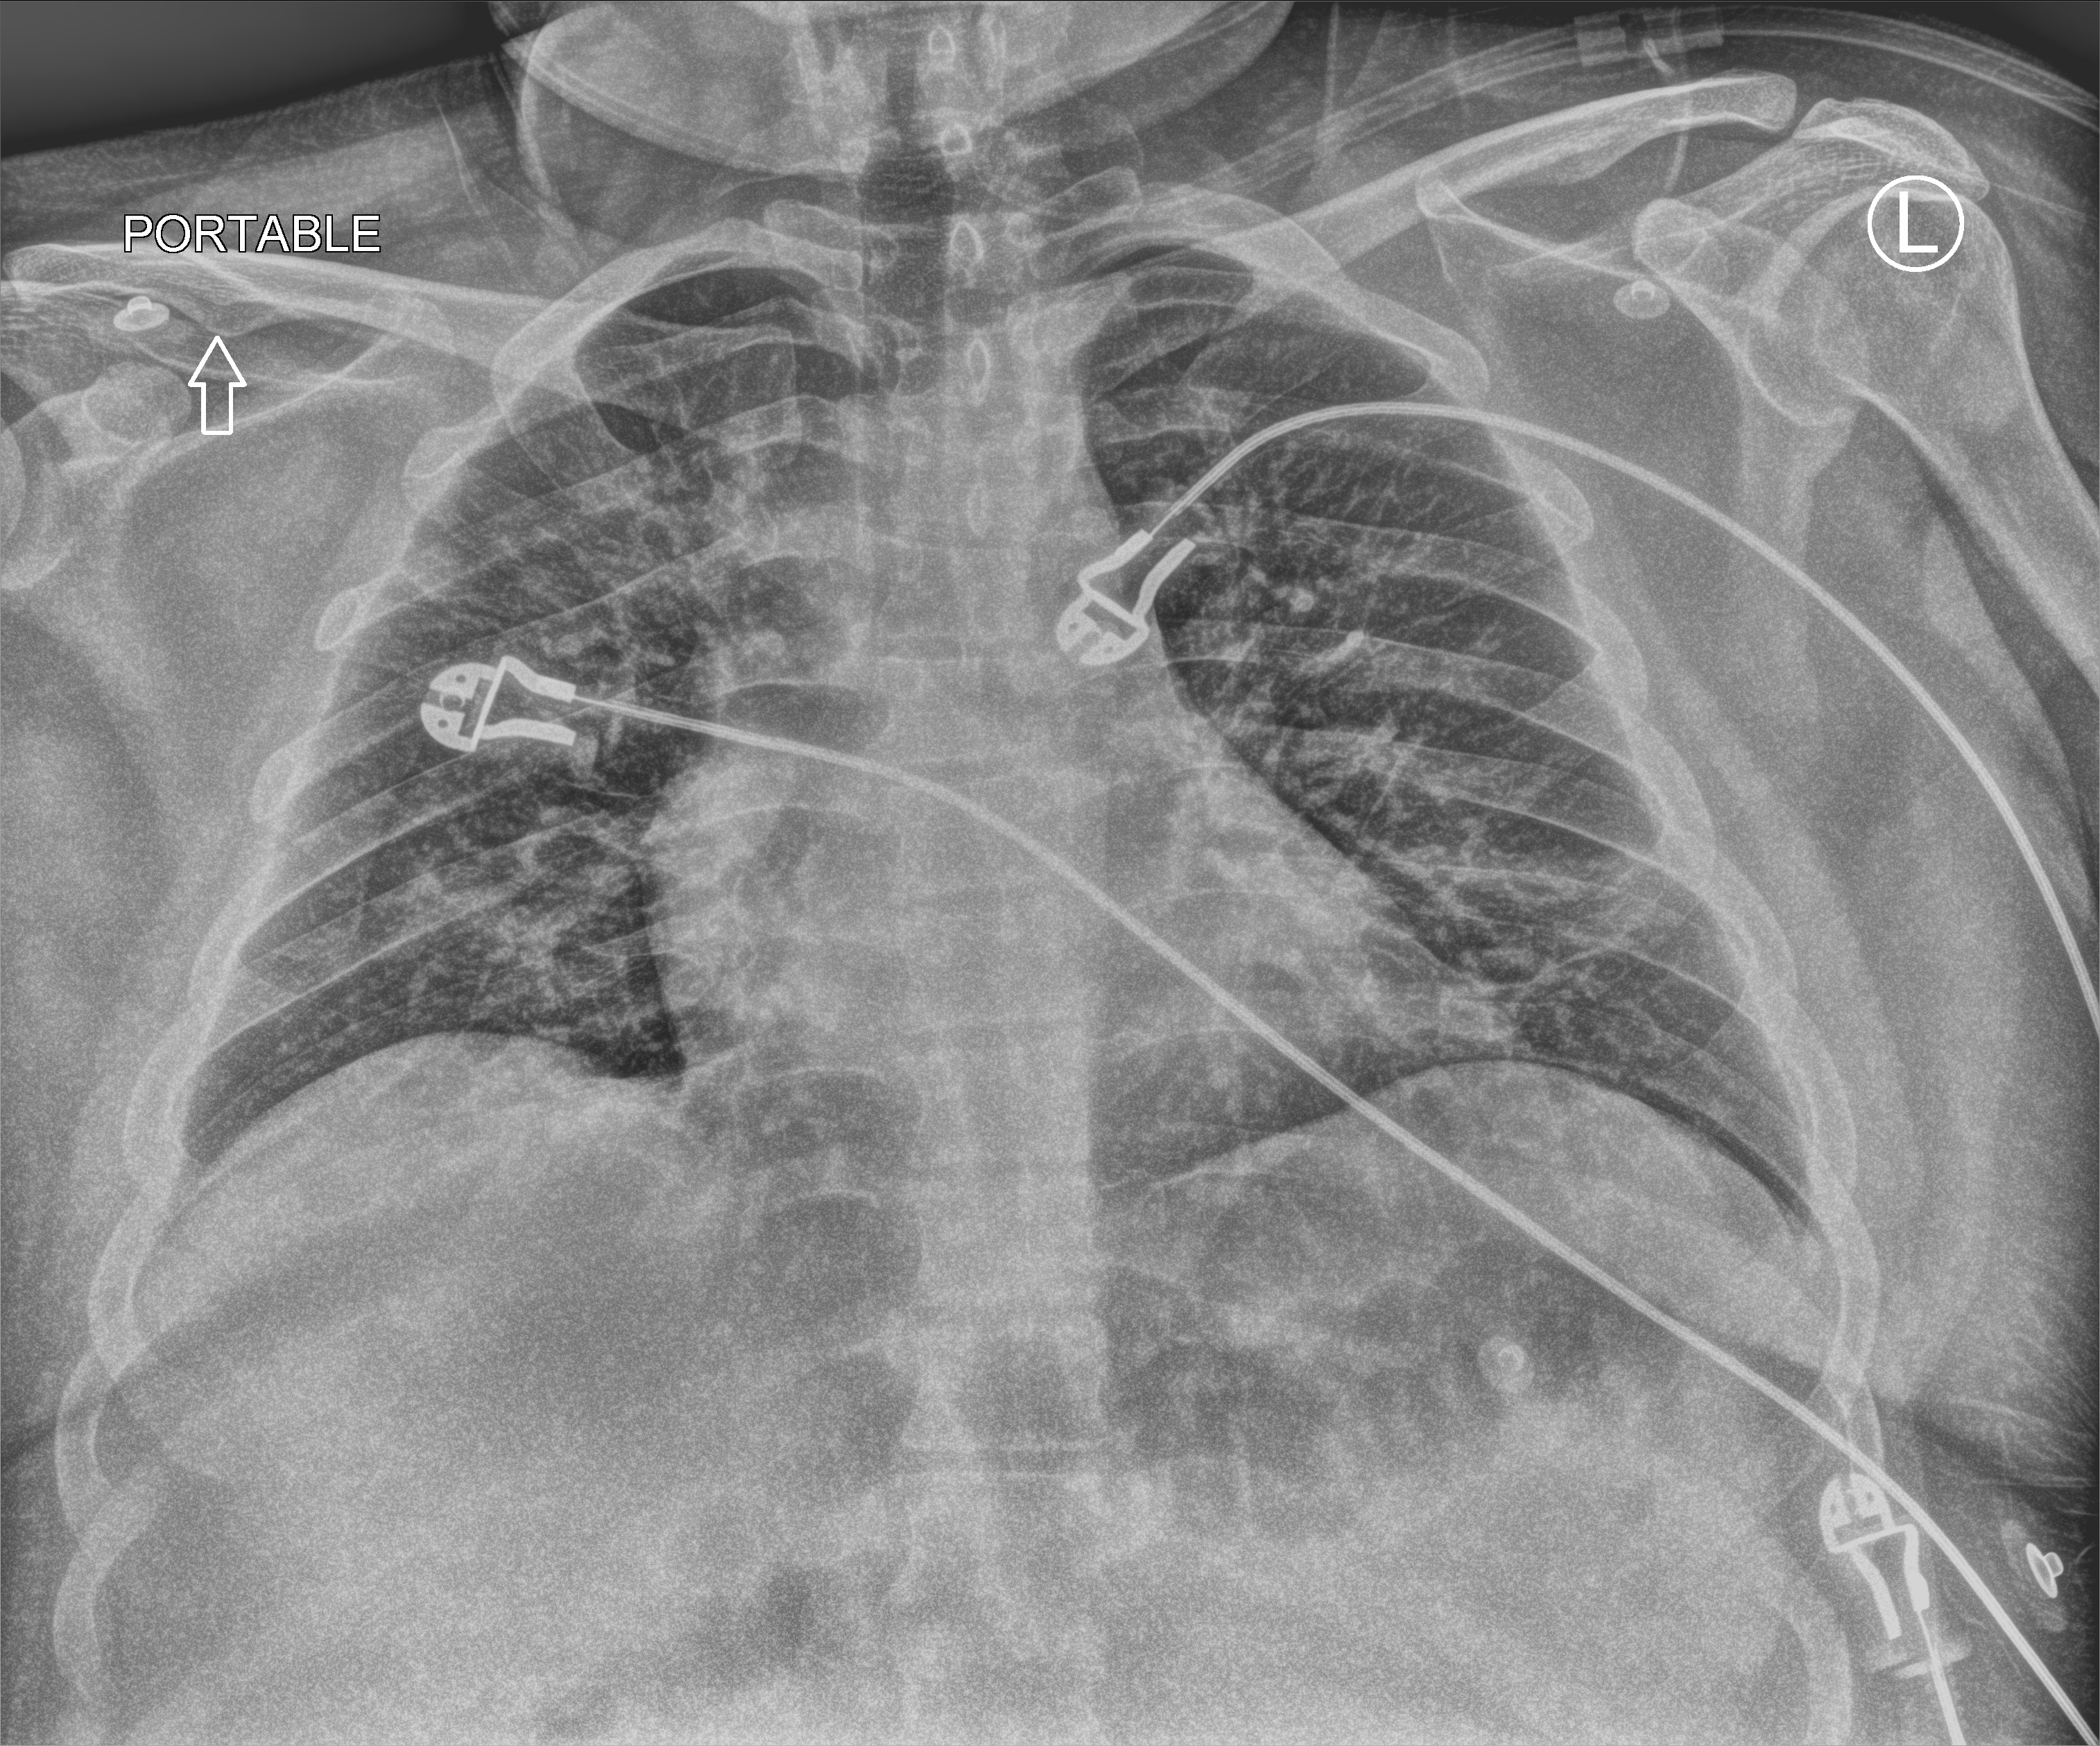
Chest X-ray (portable), anteroposterior (AP) projection. Patient hospitalised with COVID-19; male, aged 18–59 years.
From the hospital-stay record, not from the radiograph (when in the stay this image was taken is not recorded): chronic kidney disease (admission record): no; admitted to intensive care during this hospital stay: no.